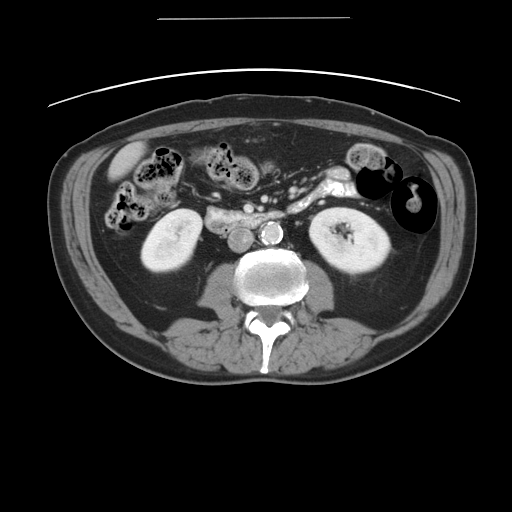
Contrast-enhanced abdominal CT, one axial slice. Slice 11 of 49 in the series (ordered by position). Reconstruction kernel STANDARD. Intravenous contrast given. Soft-tissue window (W 400 / L 40 HU). 512 × 512 image matrix. Male patient, age 57 years. From the clinical record (not read from this slice): diagnosis: colorectal cancer liver metastases, imaged before liver resection; multiple liver metastases: yes; largest metastasis: 4 cm; disease in both lobes: no.
Outlined on this slice (outlined manually by an expert reader):
- liver: box from (x=109, y=142) to (x=143, y=178) px